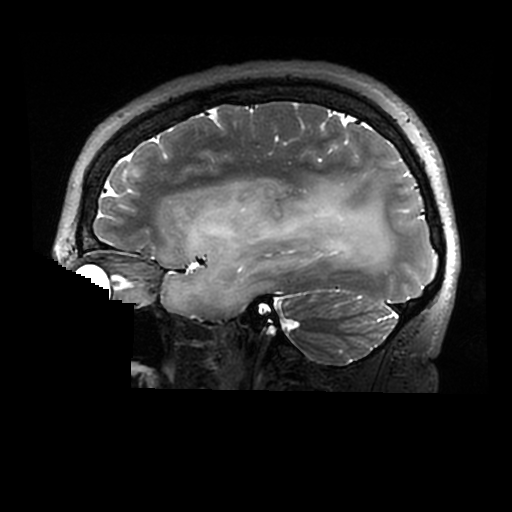
Brain MRI from a brain-tumour surgery series, one sagittal slice. Position 204 of 320 along the scan axis. 0.6 mm slice thickness. 512 × 512 image matrix, field of view 240 × 240 mm. From the clinical record (not read from this slice): histopathology: Astrocytoma; WHO grade: 2; IDH mutation: yes.
Annotated regions visible in this slice (manually delineated by an expert):
- tumour: bounding box [x1, y1, x2, y2] px = [162, 180, 392, 315]